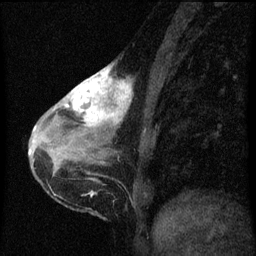
Breast MRI (dynamic contrast-enhanced), one sagittal slice. Slice 22 of 60 in the series (ordered by position). Dynamic contrast-enhanced series, image 2 of 3 at this slice position (ordered by acquisition). 1.5 T. TE 4.2 ms, TR 8 ms. 256 × 256 image matrix, field of view 180 × 180 mm. Patient: female, 38 years.
Outlined on this slice (semi-automatic segmentation, software-assisted and operator-edited):
- analysis volume of interest (the breast-tissue region the enhancement analysis was run in; not a lesion): bounding box [x1, y1, x2, y2] px = [61, 64, 134, 147]
- tumour enhancement mask (voxels above the 70 % enhancement threshold inside the analysis volume of interest): [62, 64, 132, 127]